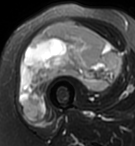
MRI of an extremity soft-tissue mass, one axial slice. Slice 43 of 95 in the series (ordered by position). T2-weighted fat-saturated. MR volume resampled by the dataset authors to the PET/CT grid (not the native acquisition matrix). 135 × 146 image matrix, field of view 132 × 143 mm. Female patient. From the clinical record (not read from this slice): histological type: pleiomorphic undifferentiated sarcoma; grade: high; site of the primary tumour: right quadricep.
Annotated regions visible in this slice (expert contour drawn on MRI and transferred to this co-registered scan by the dataset authors):
- gross tumour volume including surrounding oedema: bounding box [x1, y1, x2, y2] px = [21, 20, 122, 121]
- gross tumour volume (mass): [21, 20, 122, 121]